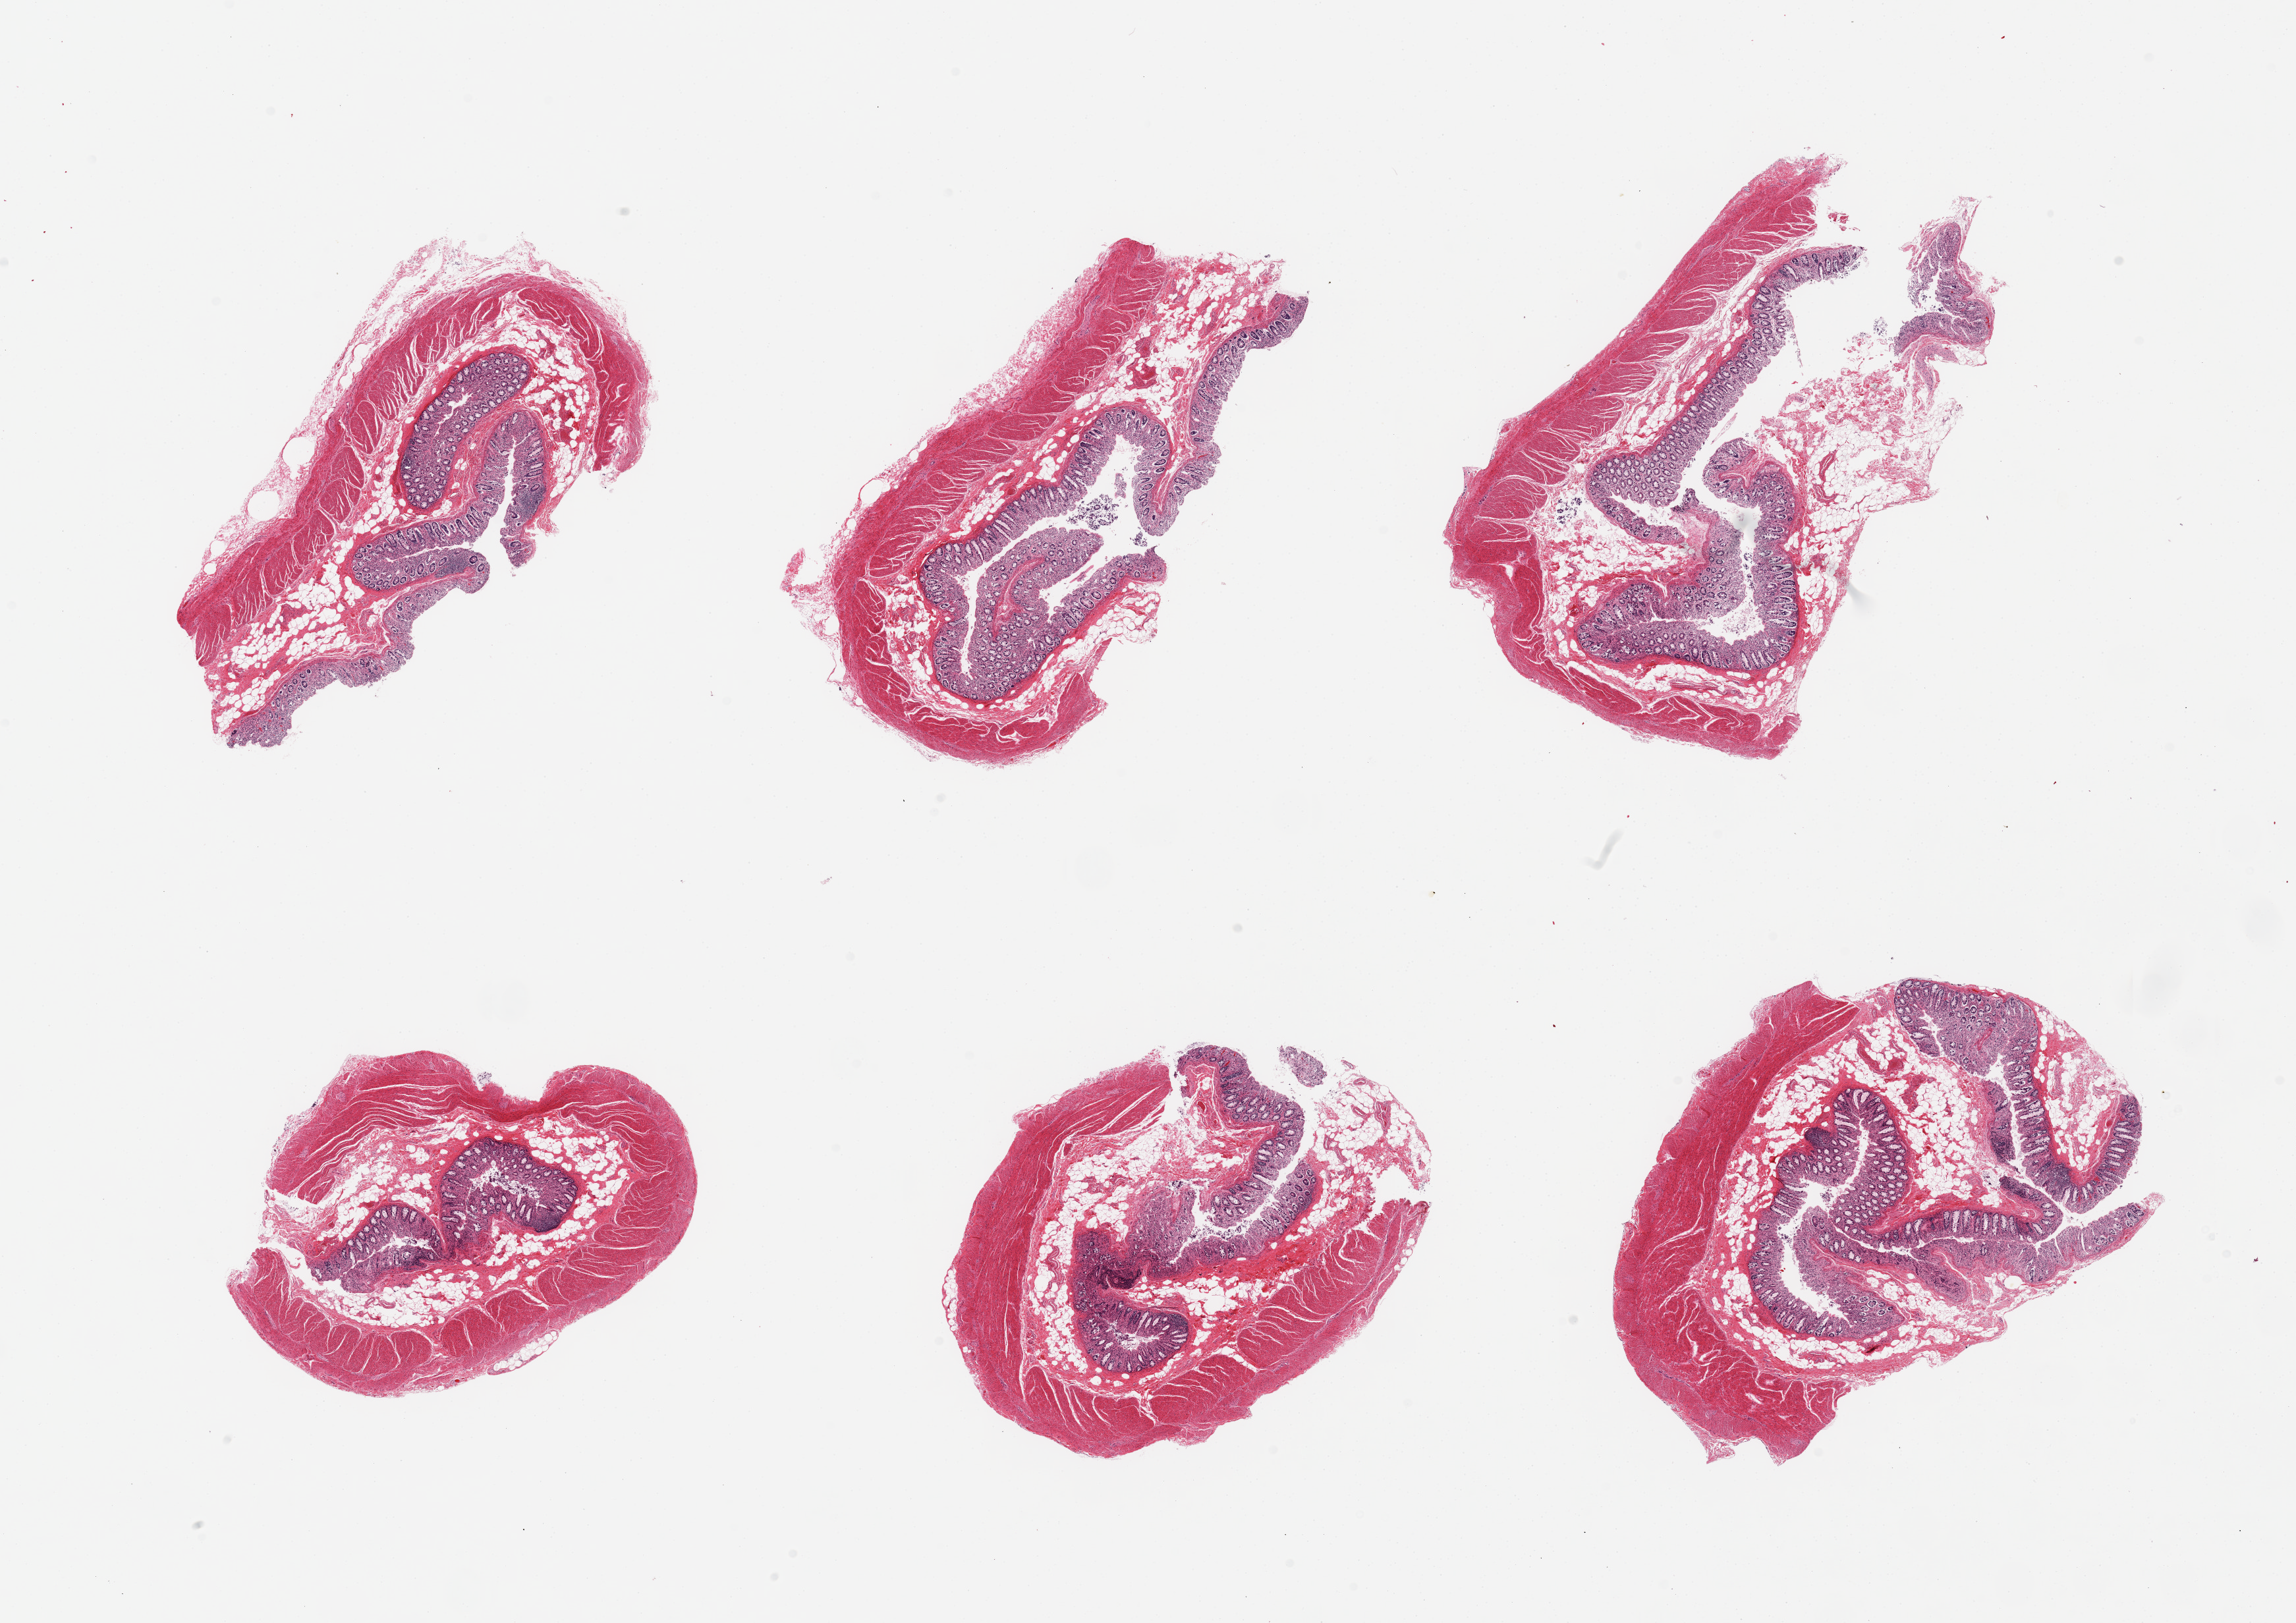
Digitized H&E-stained section, brightfield, a low-resolution overview of the entire scanned area, about 27.6 x 19.5 mm (slide scanned at 20x). PAXgene-fixed, paraffin-embedded tissue. Section of transverse colon (target tissue). Donor tissue sample. Donor: male.
• review note (as recorded): 6 pieces; well dissected; mucosa poorly preserved, muscle better